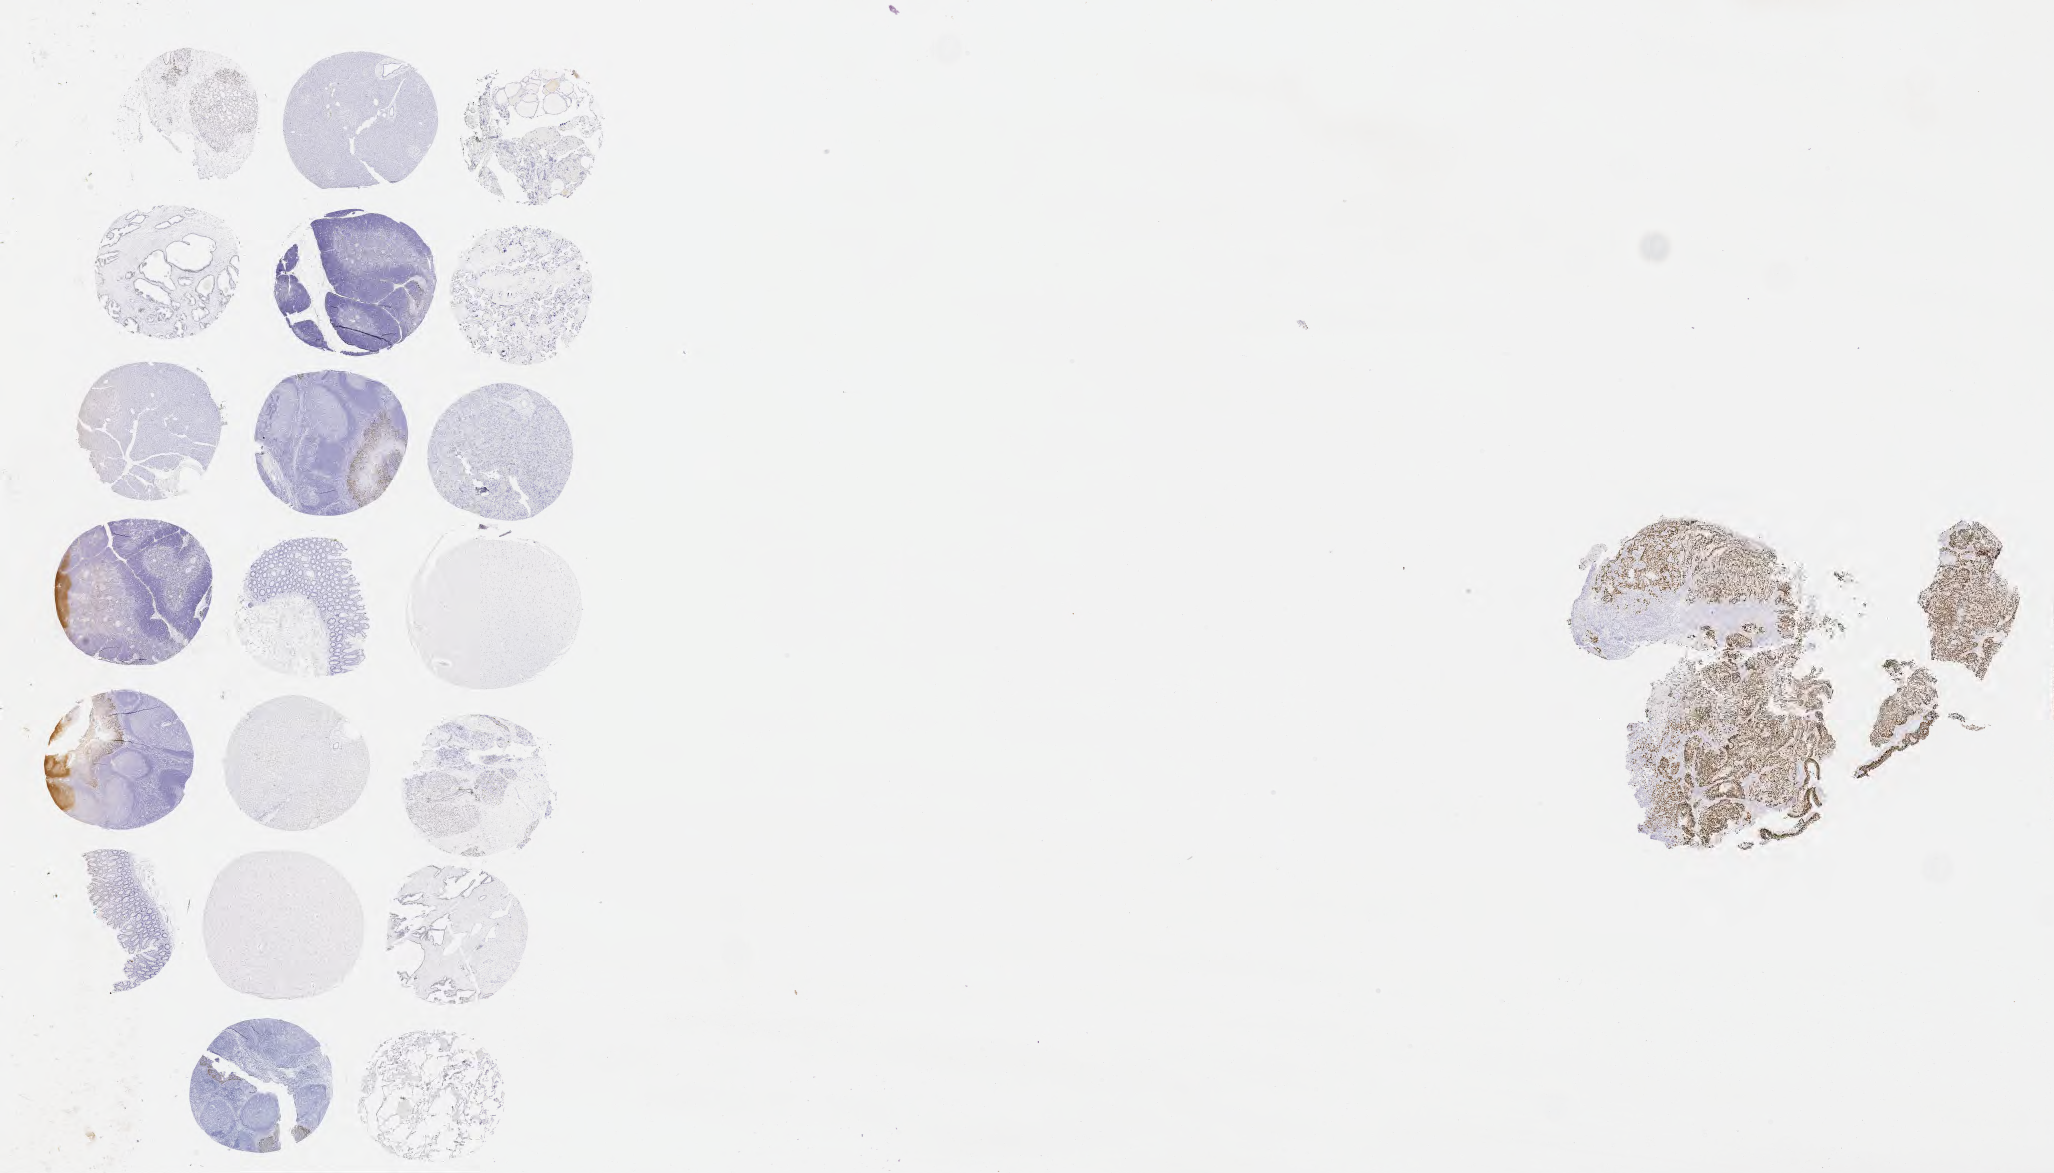
Whole-slide image, immunohistochemical stain for p40 — low-resolution overview of the scanned area, about 33.2 x 19.0 mm. Tumor tissue. Anatomic site: cervix. Patient: female, aged 56.
Histologic diagnosis: Adenocarcinoma, NOS.